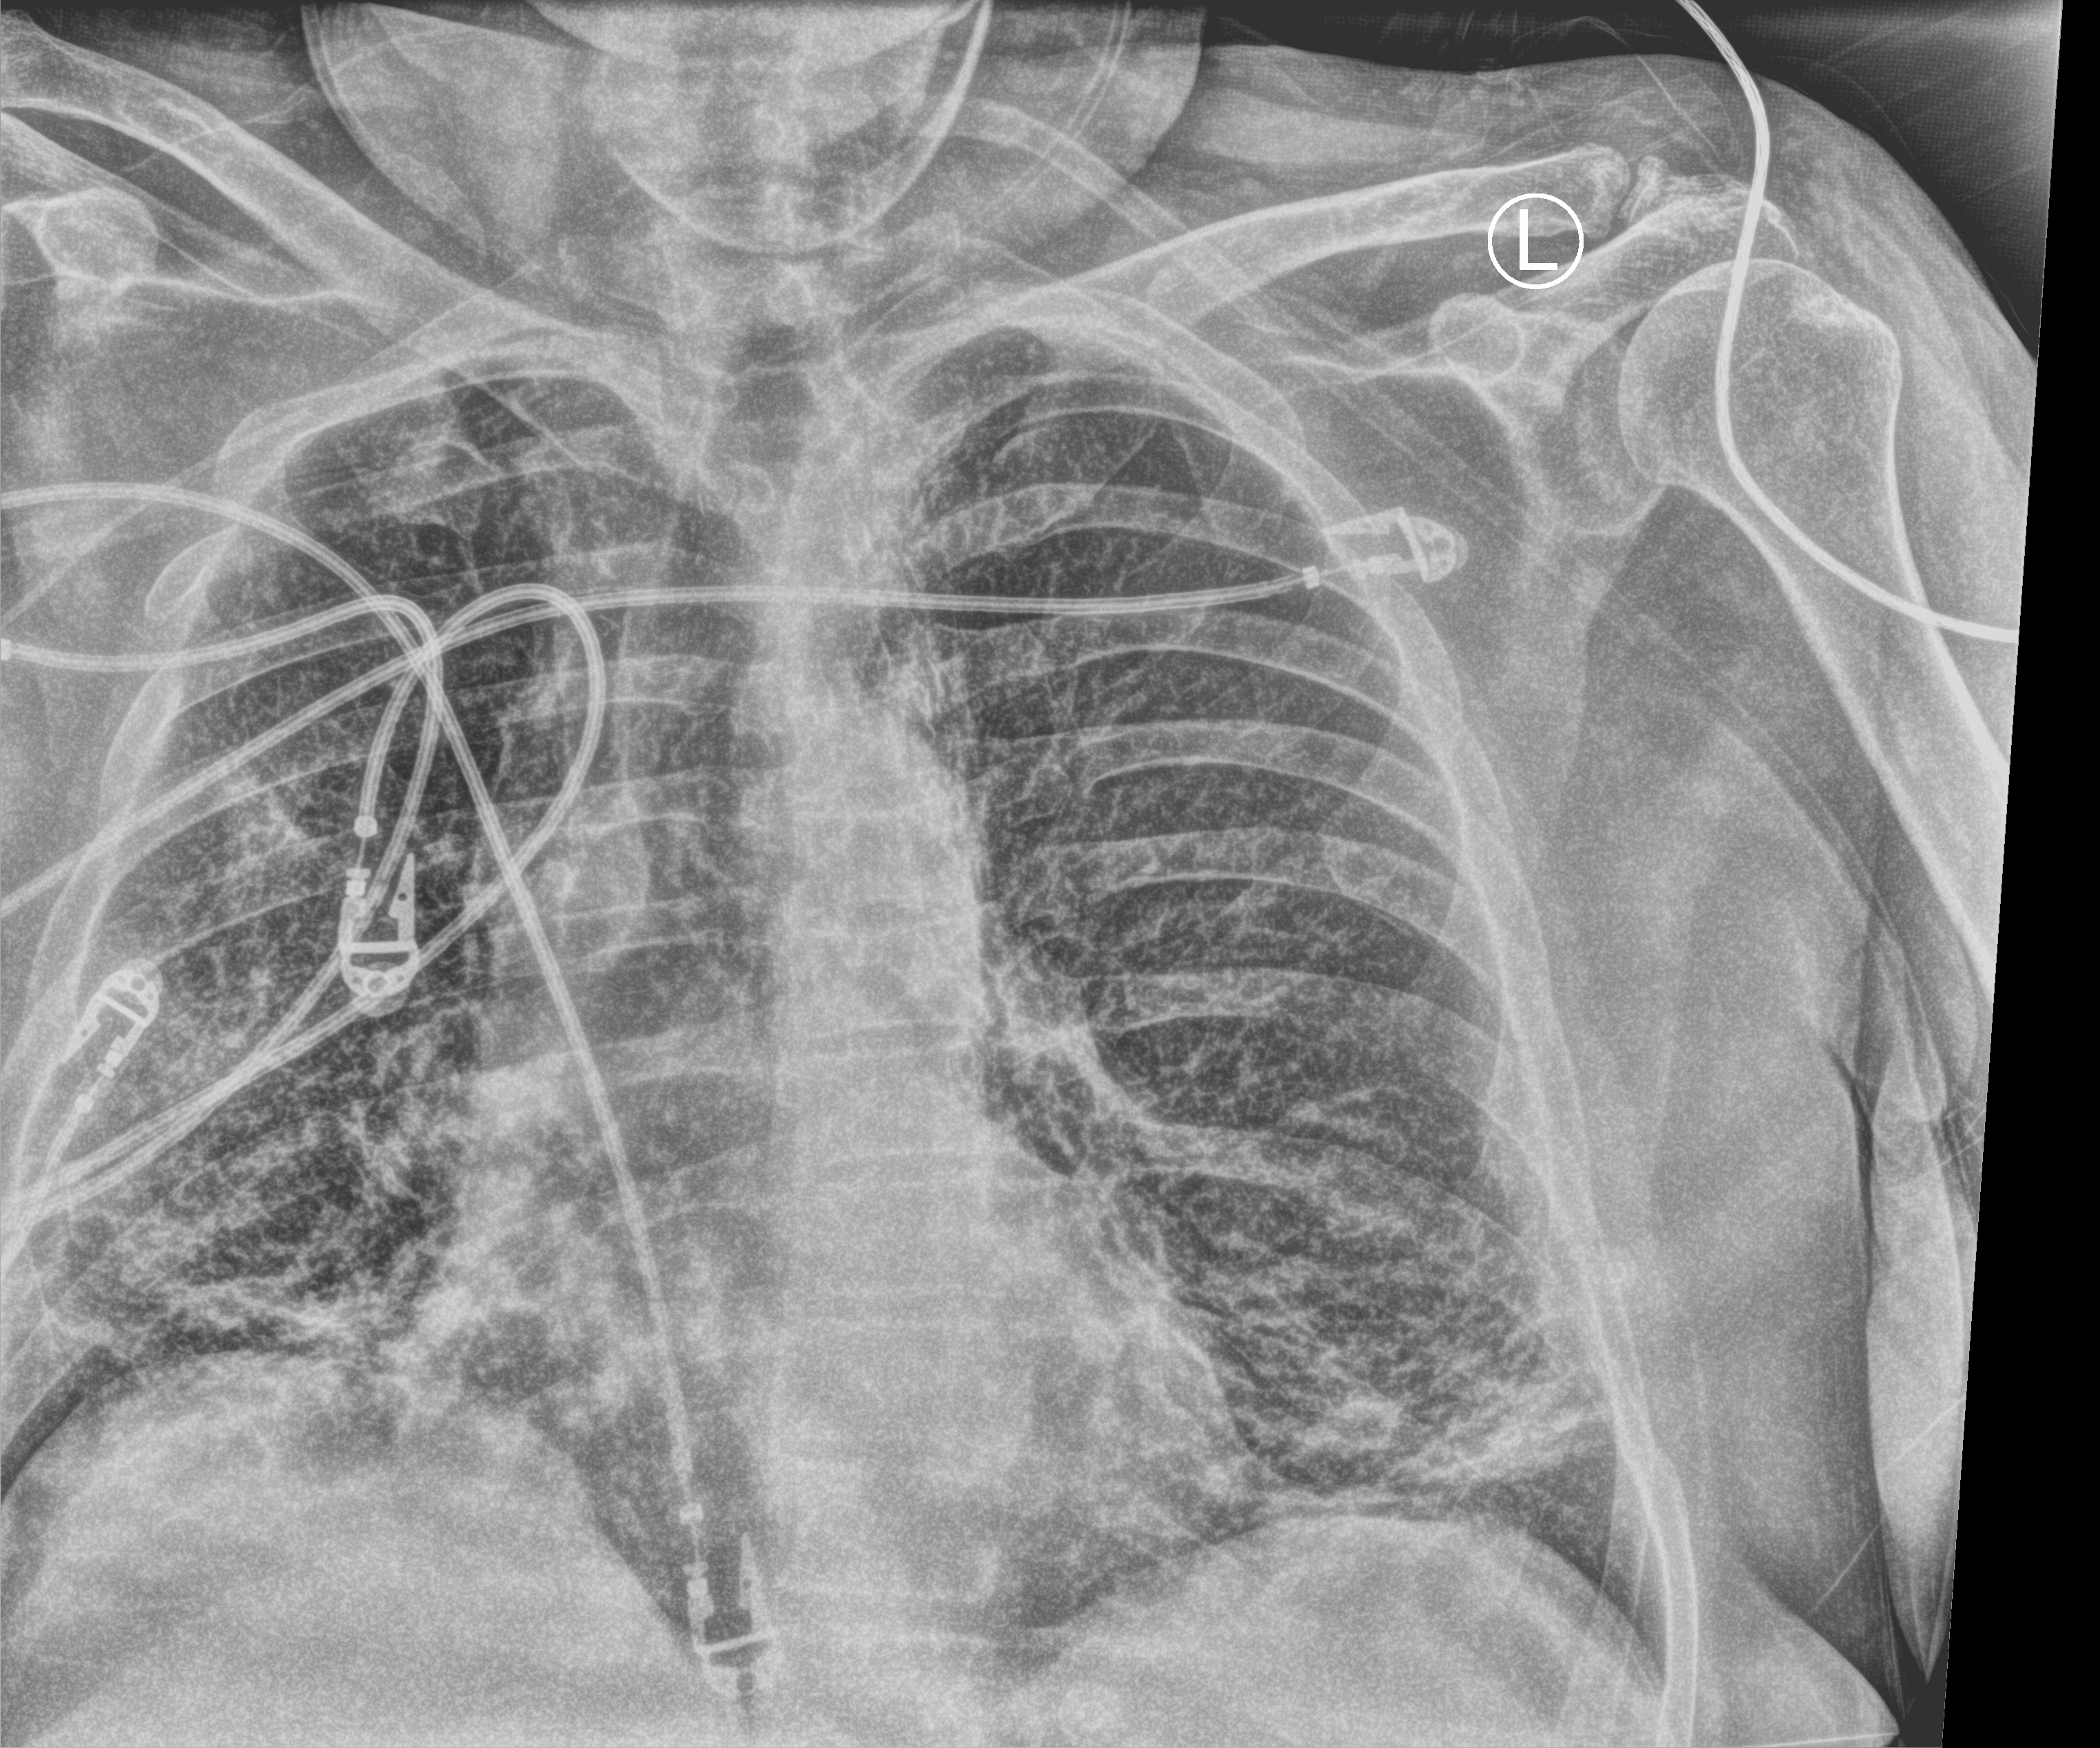
Chest X-ray (portable); anteroposterior (AP) projection. Patient hospitalised with COVID-19; male, aged 60–74 years.
Admission-level facts for this patient (not findings on this image; timing relative to this image not recorded): admitted to intensive care during this hospital stay: no; hypertension (admission record): no.